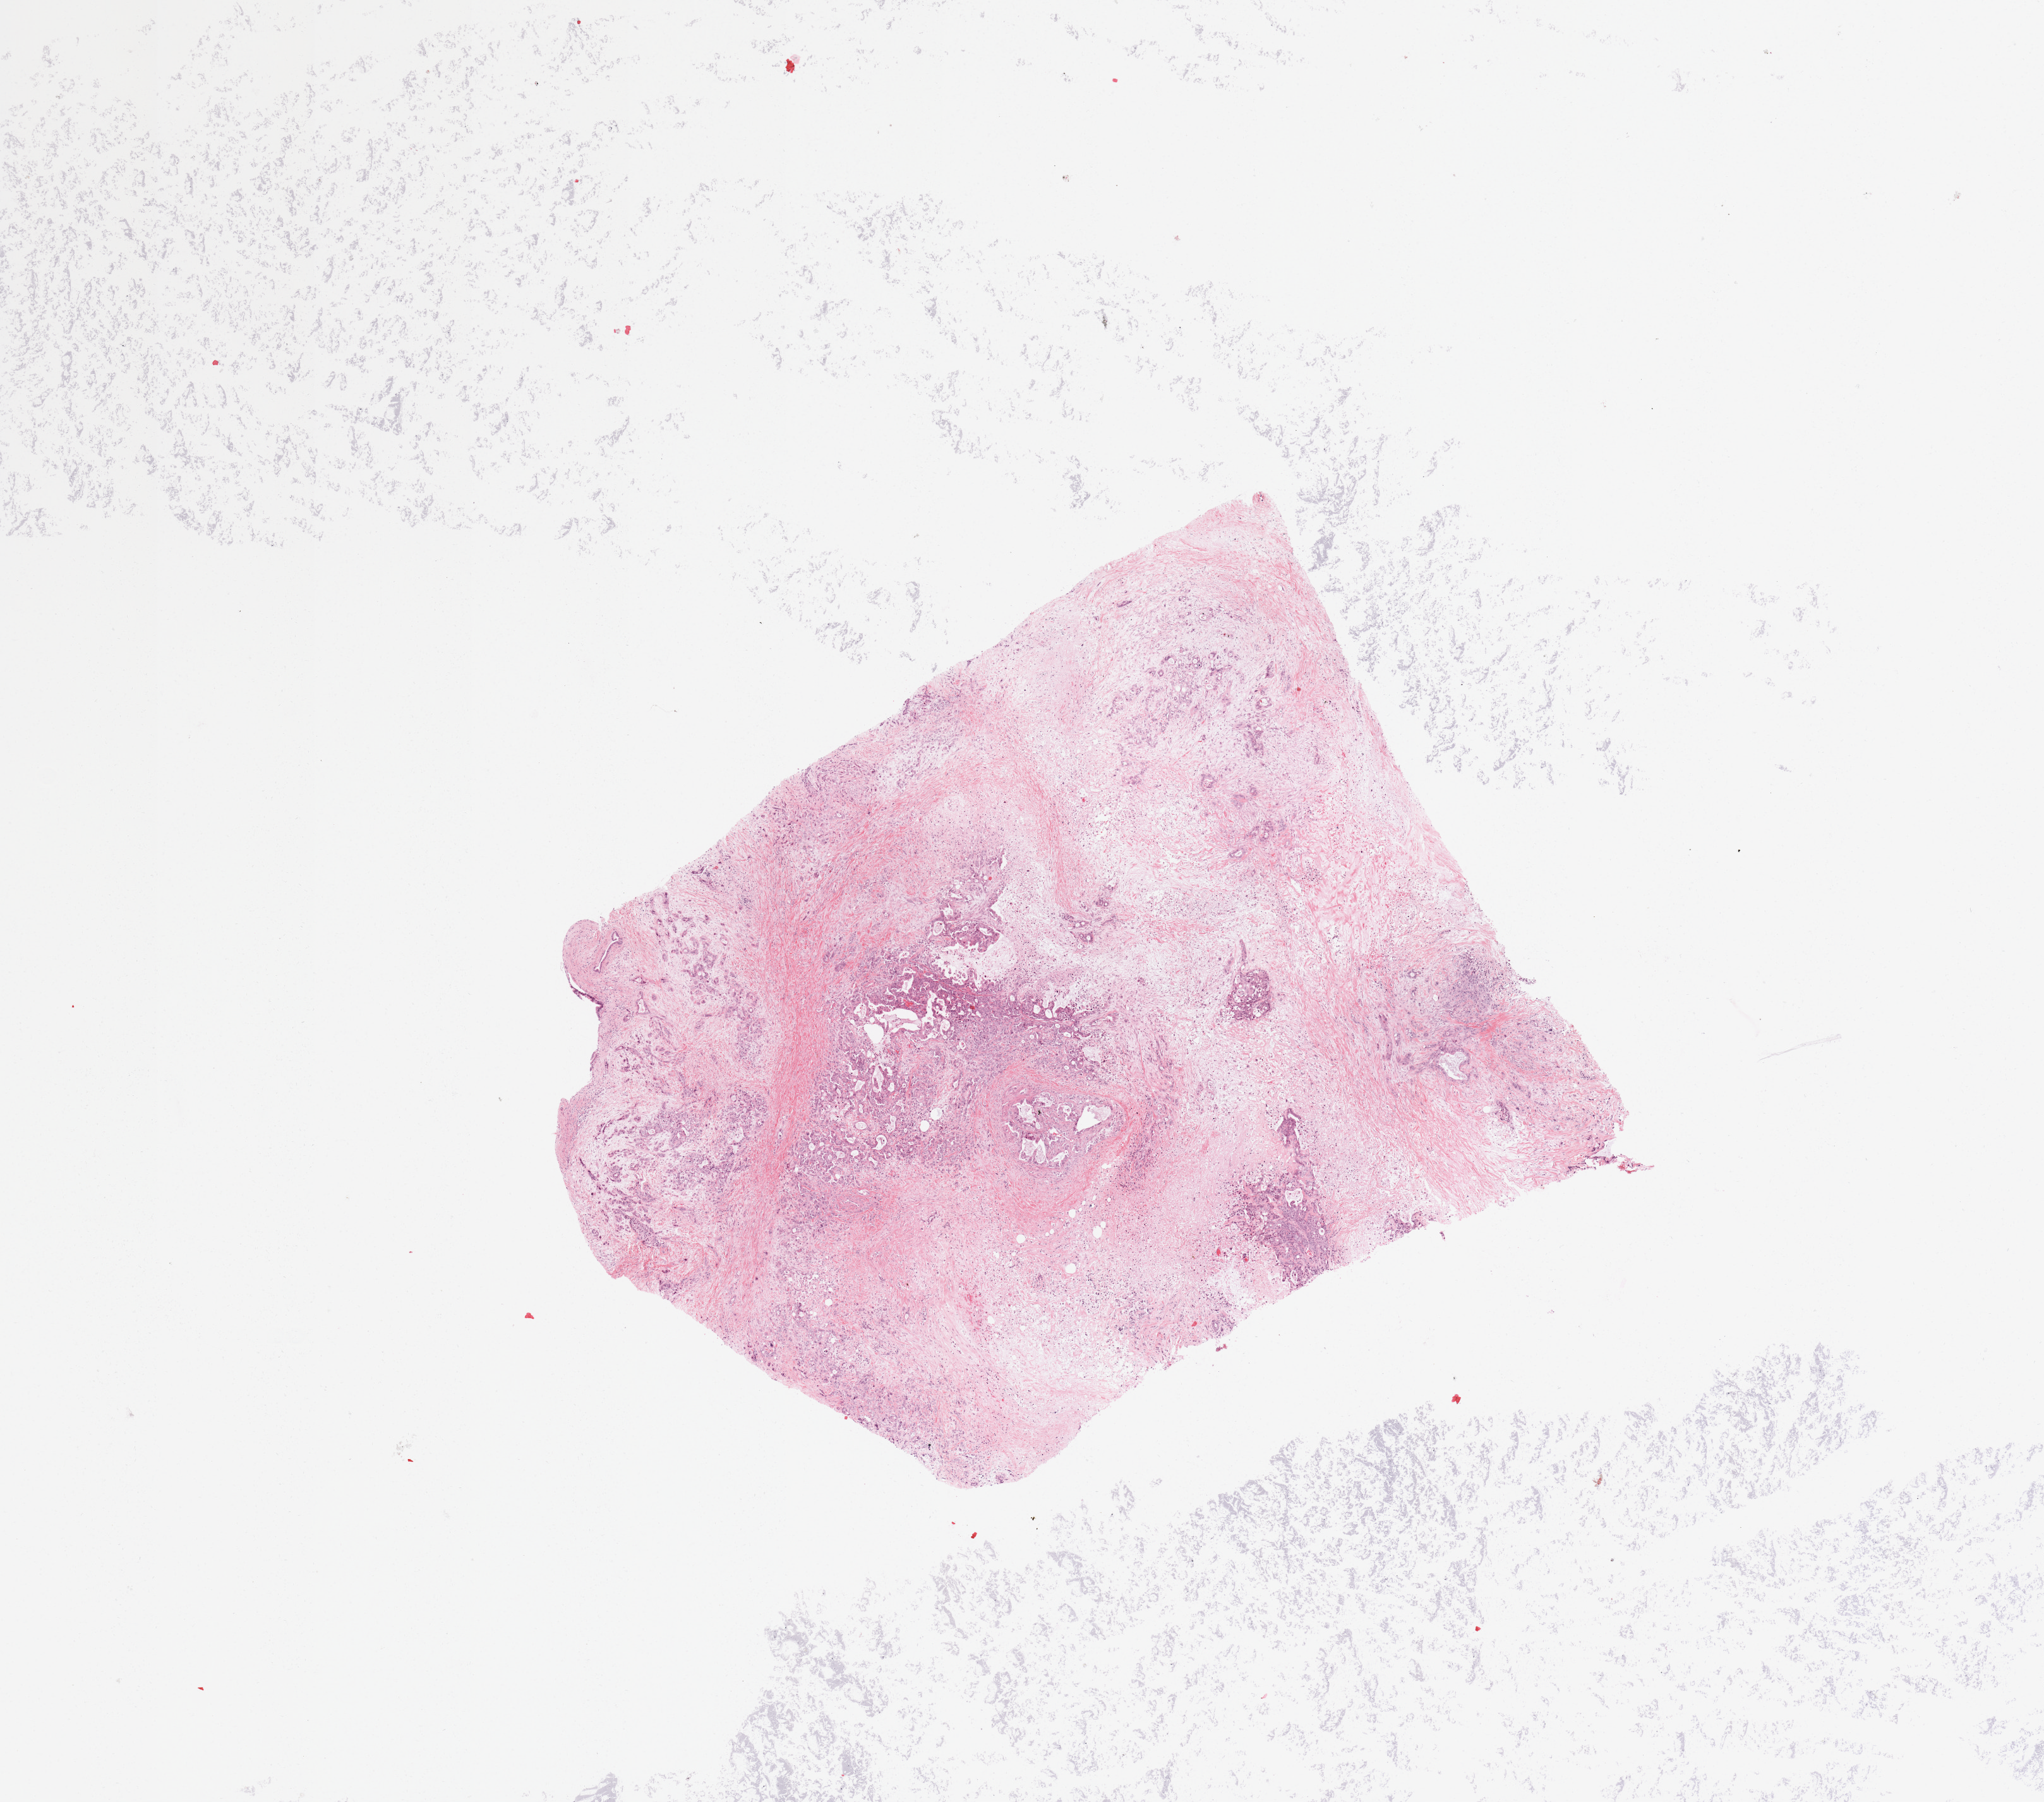
Digitized H&E-stained tissue section (whole slide), a low-resolution overview of the entire scanned area, about 12.8 x 11.3 mm, tumour tissue sample, sampled site: pancreas. 46-year-old male patient. Histologic grade: G3 (poorly differentiated). Composition of this section per pathologist review: tumour nuclei 40%, necrosis 10%.
AJCC pathologic stage: IIB. Histologic diagnosis: Infiltrating duct carcinoma, NOS.